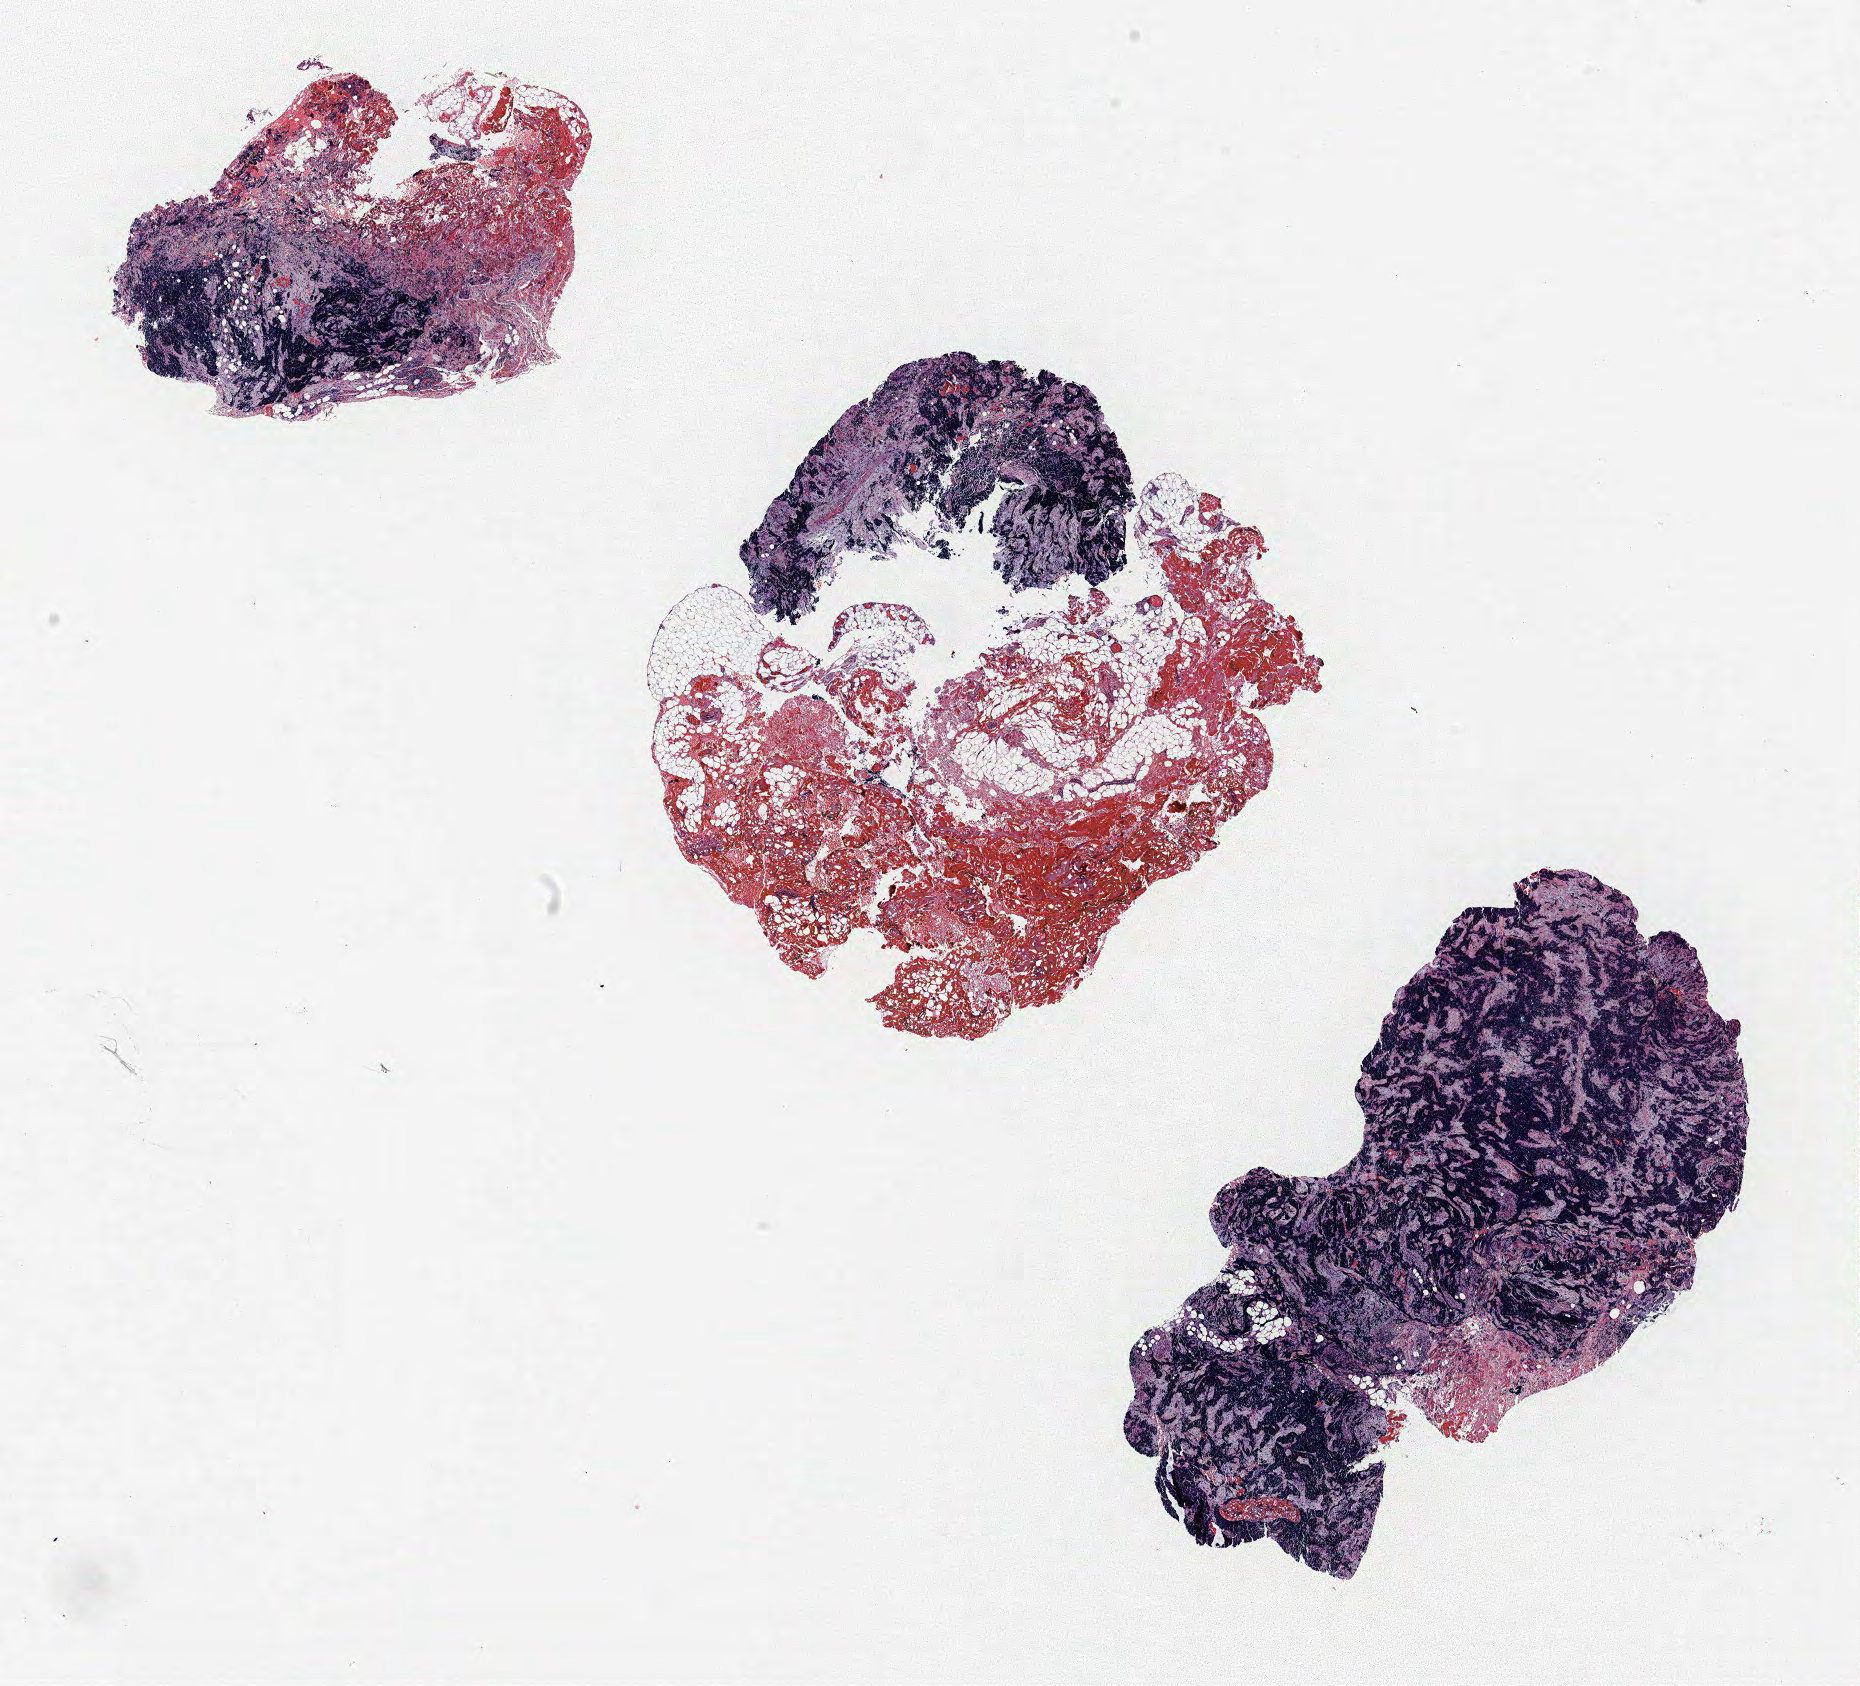
Whole-slide histology image, H&E-stained, whole scanned area (about 14.9 x 13.5 mm, slide scanned at 40x) shown as a low-resolution overview. FFPE section. Lung. Female patient, aged 63 at enrolment. Current smoker at enrolment. Grade: undifferentiated (G4).
• stage (AJCC 6th edition): IIIB
• primary tumour location (clinical record): right upper lobe
• participant's lung-cancer diagnosis: Oat cell carcinoma